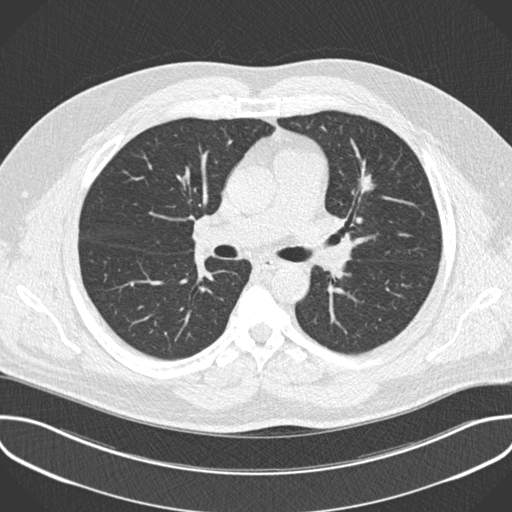
Low-dose screening chest CT, one axial slice; position 129 of 201 along the scan axis; reconstruction kernel B30f; lung window (W 1500 / L -600 HU); 2 mm slice thickness; 512 × 512 image matrix.
Outlined on this slice (outlined manually by an expert reader):
- lesion 1 (tumor, upper lobe of left lung): bounding box [x1, y1, x2, y2] px = [361, 171, 374, 192]